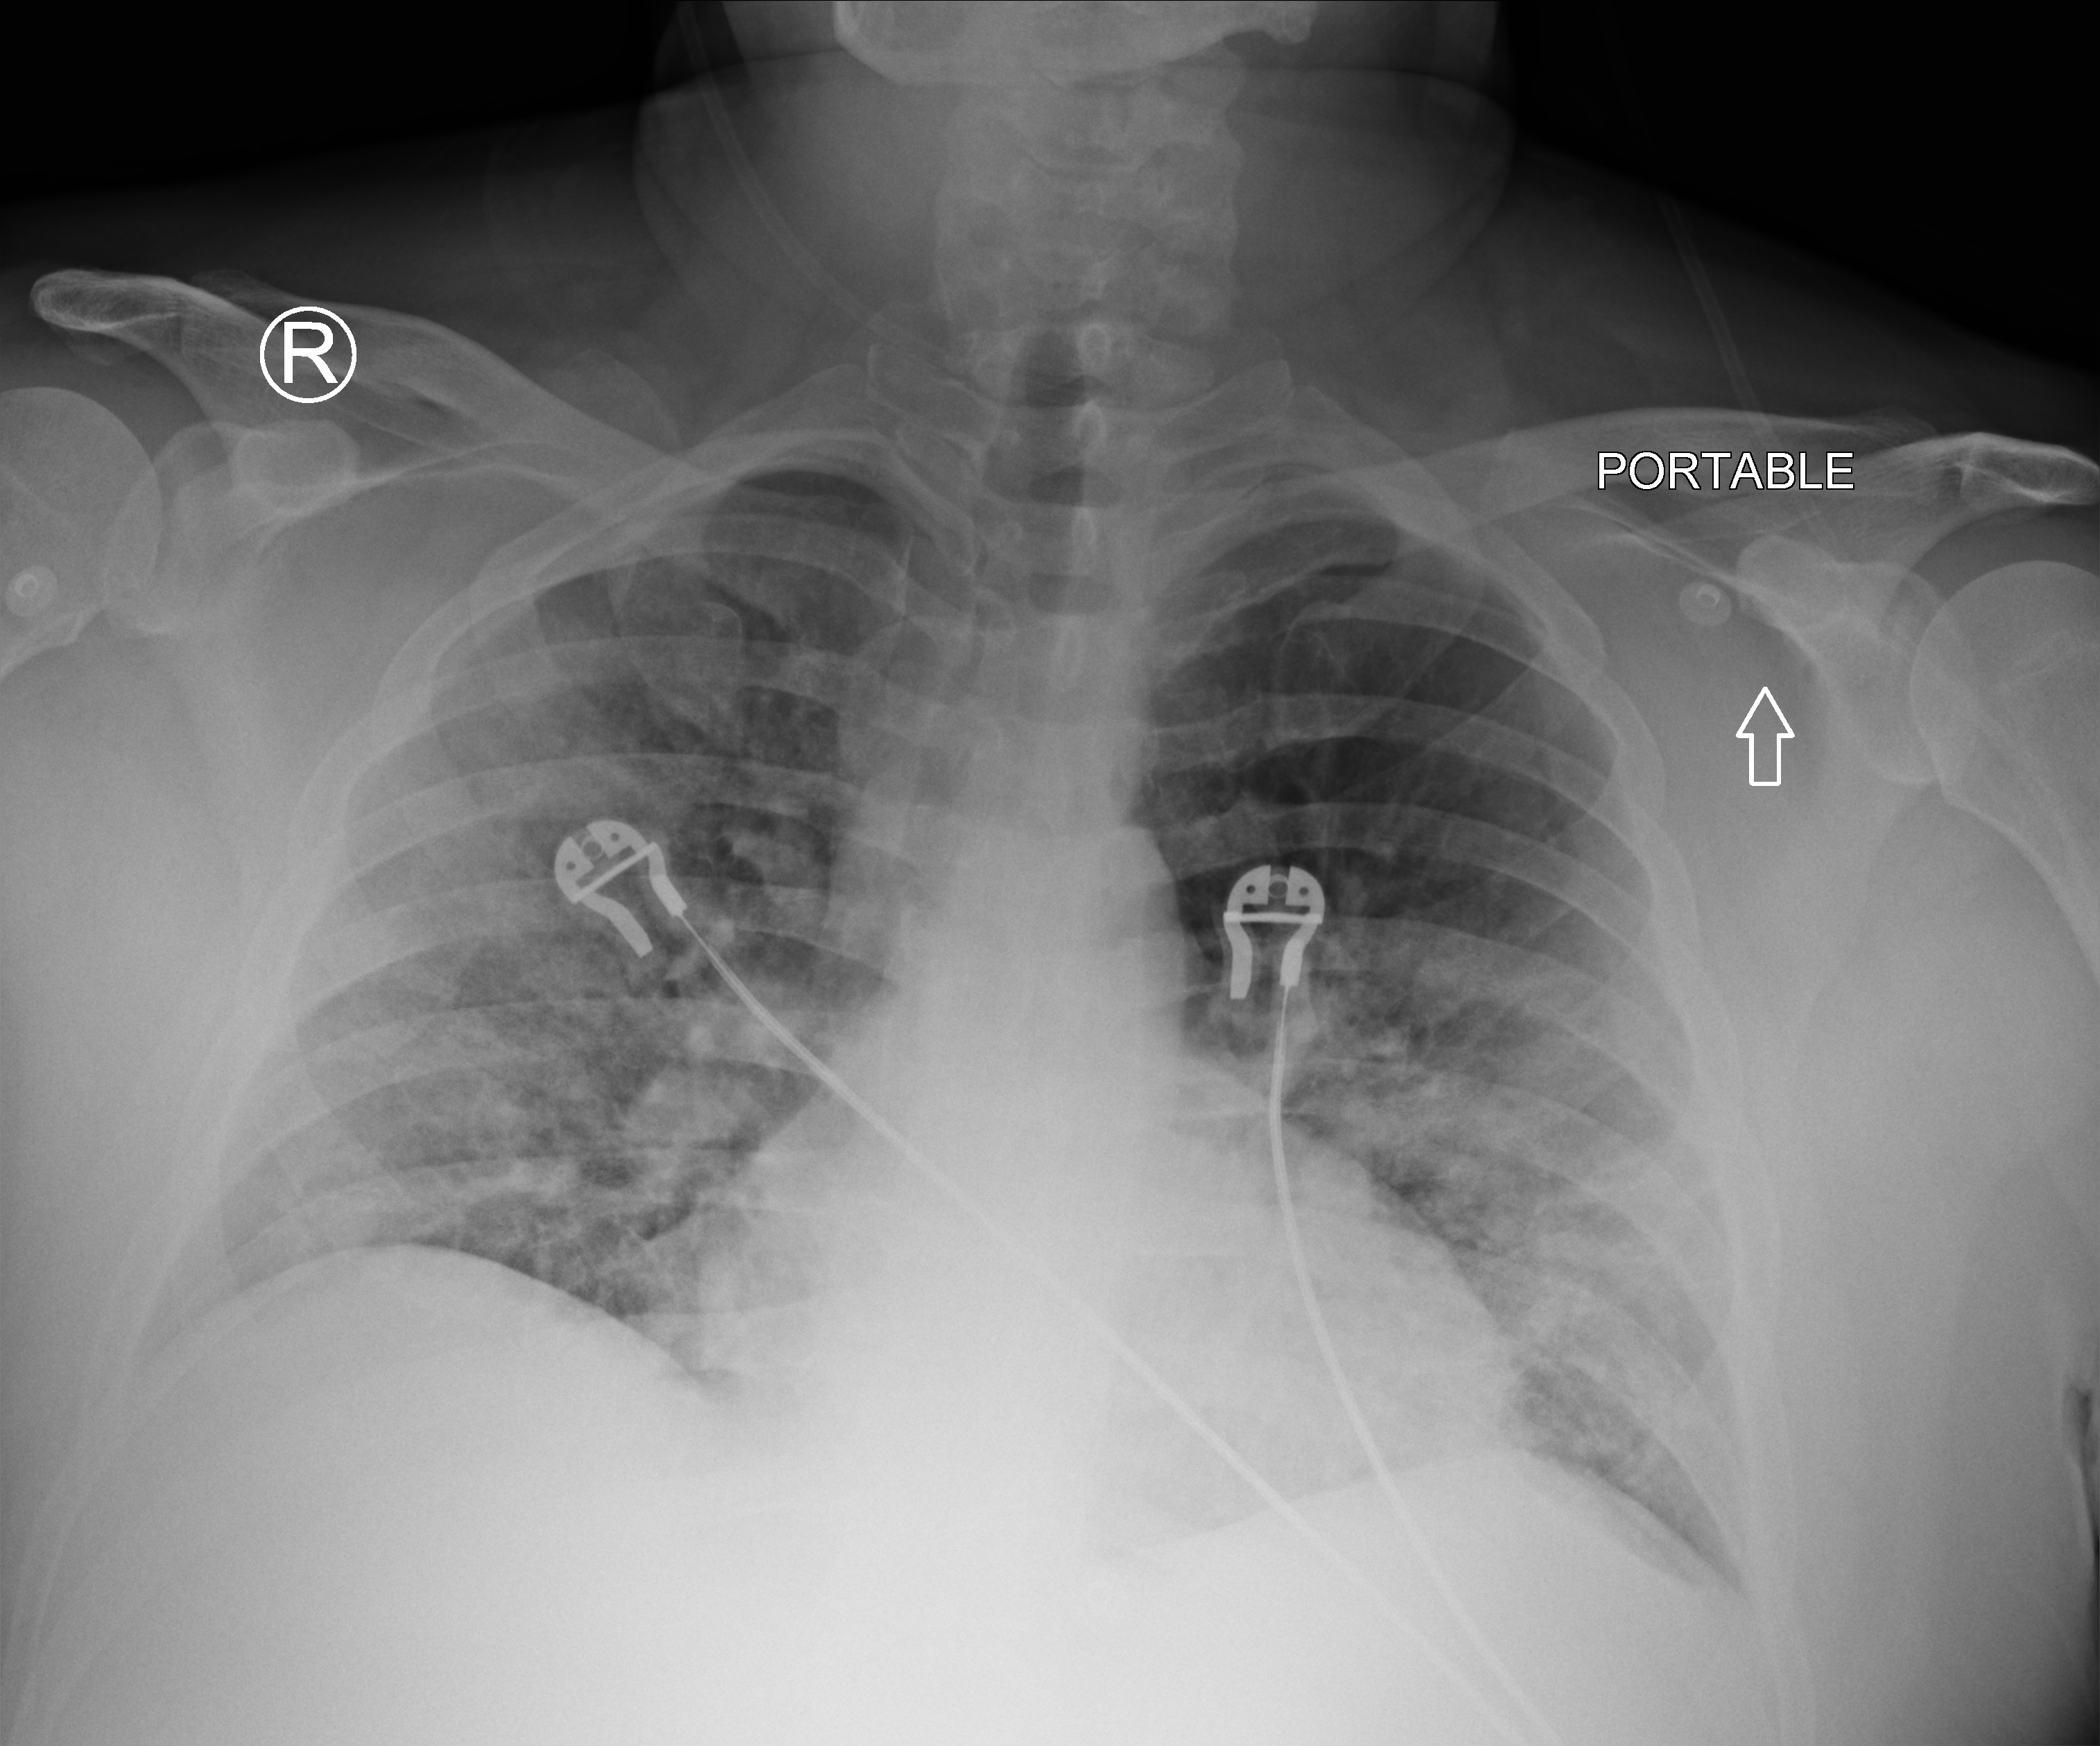
Bedside chest radiograph (computed radiography); anteroposterior (AP) projection. Male patient hospitalised with COVID-19, age 18–59 years.
Admission-level facts for this patient (not findings on this image; timing relative to this image not recorded): admitted to intensive care during this hospital stay: yes; mechanically ventilated during this hospital stay: yes; COPD (admission record): no.